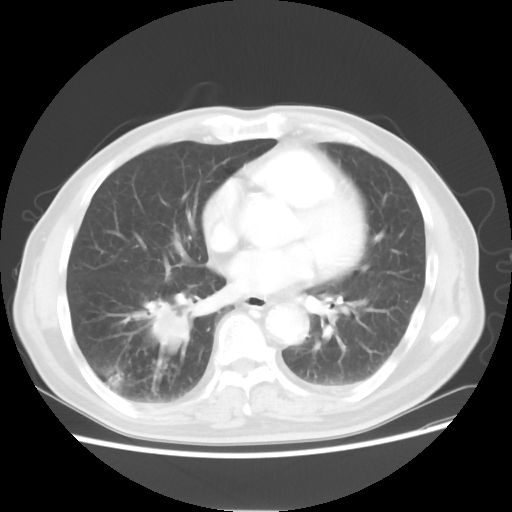
Chest CT, one axial slice. Slice 27 of 58 in the series (ordered by position). Reconstruction kernel STANDARD. Lung window (W 1500 / L -600 HU). 512 × 512 image matrix. Patient: male, 74 years. From the clinical record (not read from this slice): clinical TNM (as recorded): T1c N1 M1.
Annotated regions visible in this slice (bounding box drawn by a radiologist):
- lung tumour (recorded histology: adenocarcinoma): bounding box <117,289,195,368> (left, top, right, bottom; pixels)